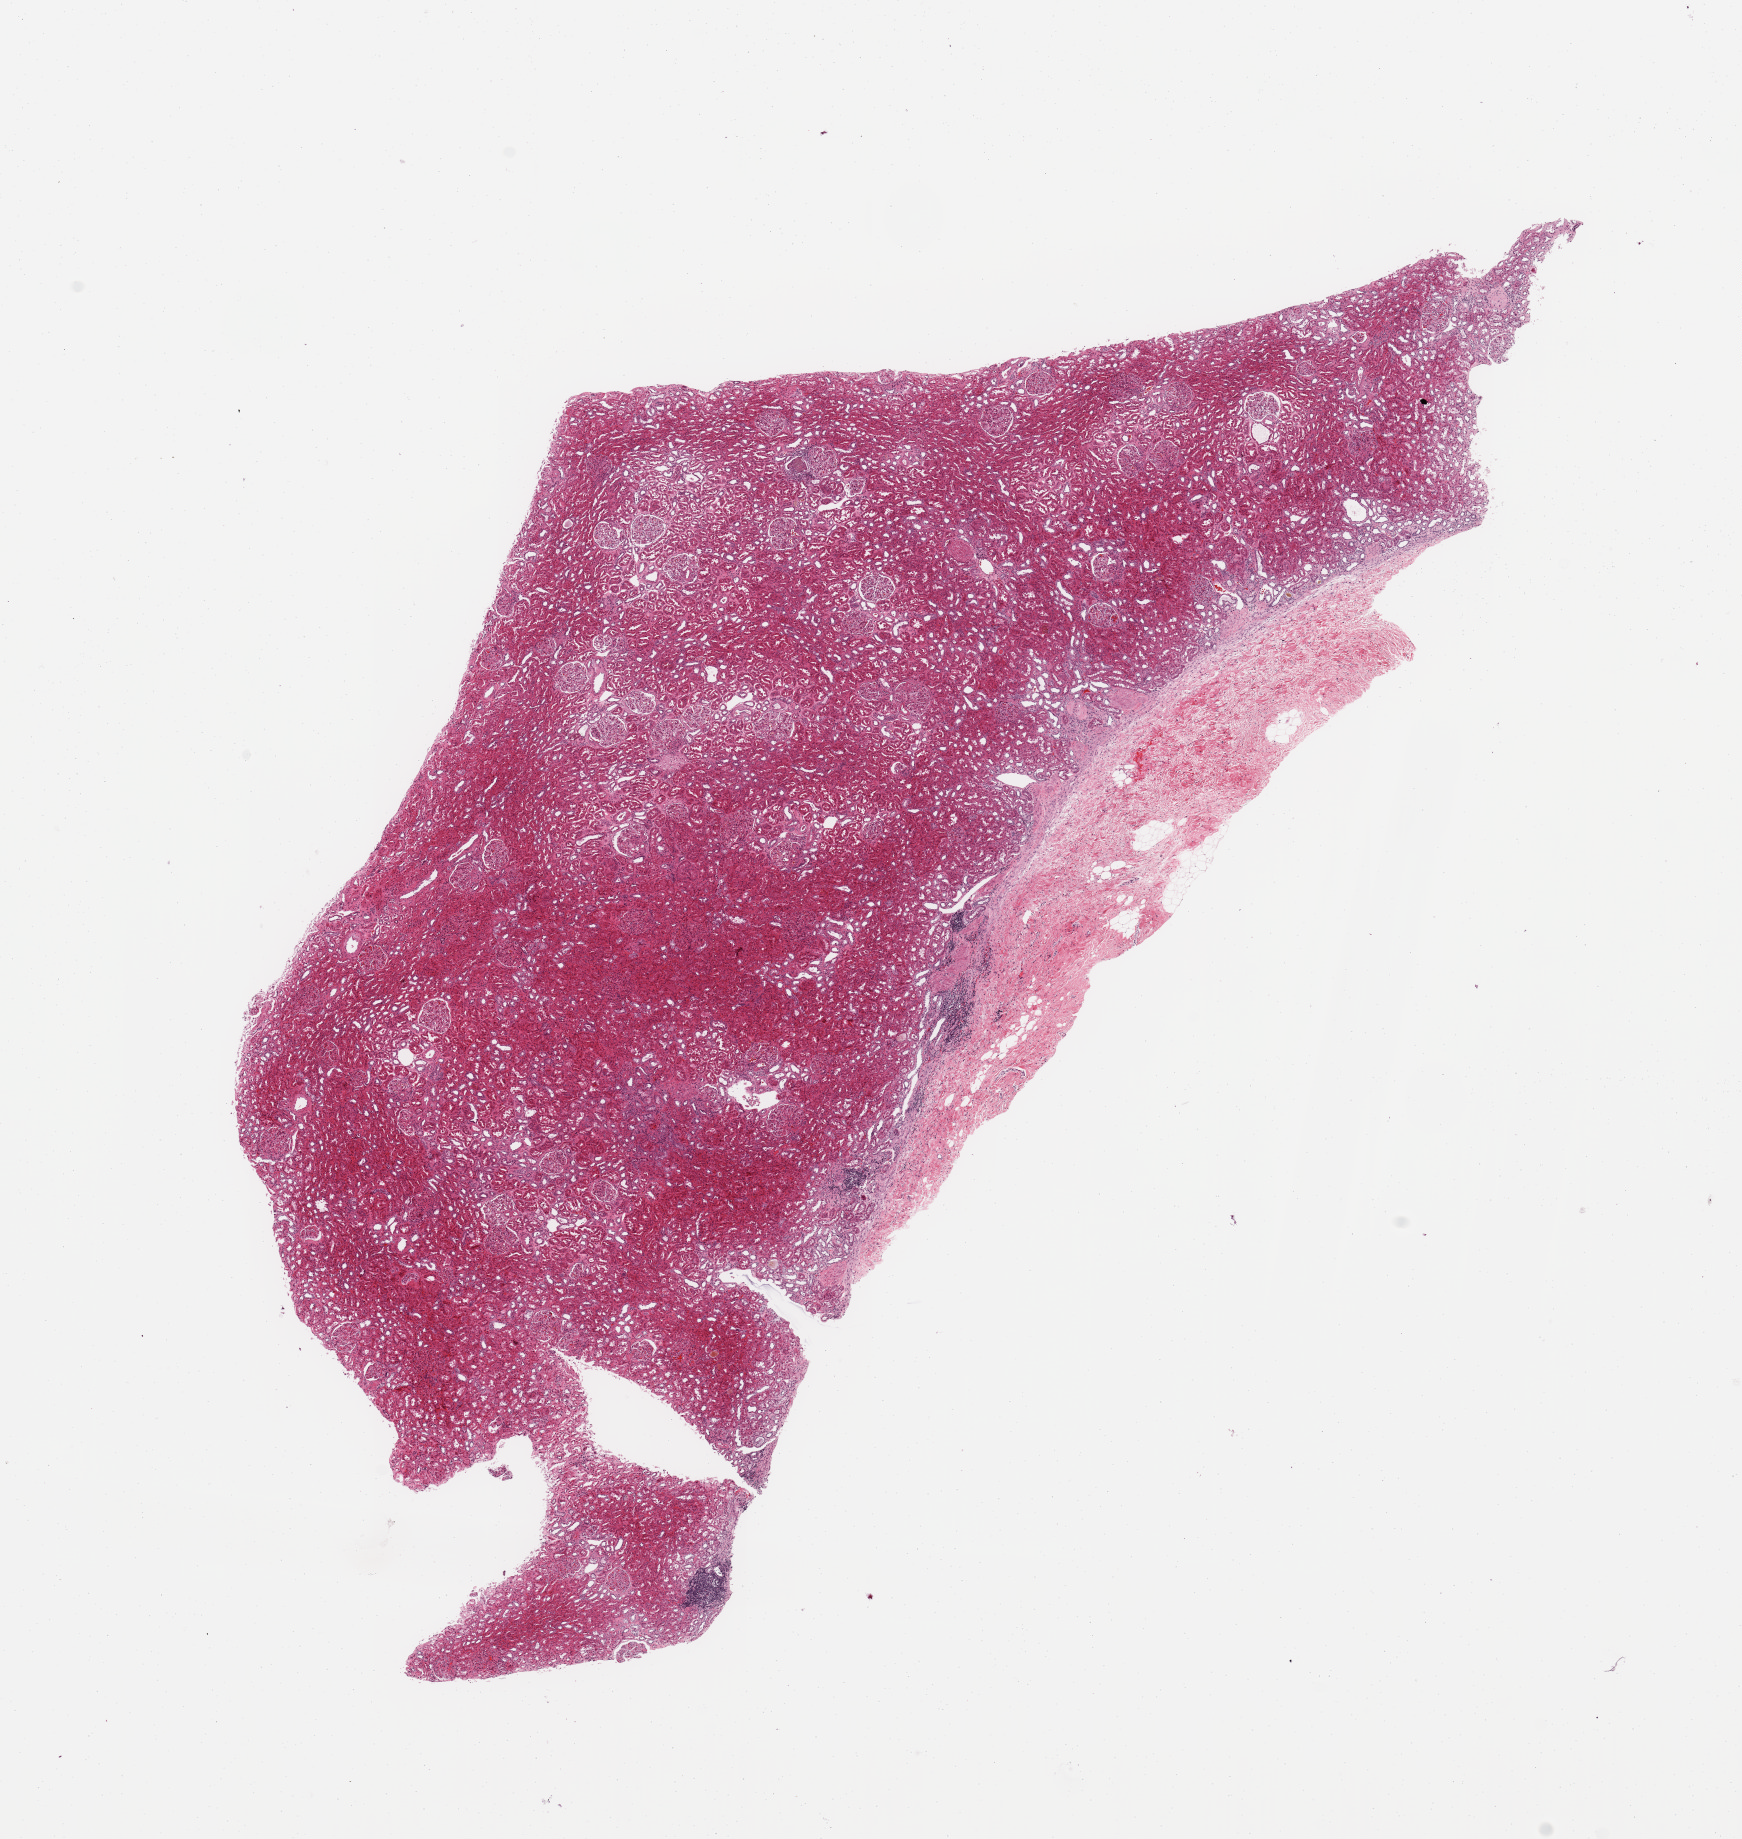
Whole-slide histology image, H&E, whole scanned area (about 13.8 x 14.5 mm, acquisition: 20x scan) shown as a low-resolution overview, normal (non-tumour) tissue sample, sampled site: kidney. Patient: male, age 48 years.
This section: normal (non-tumour) tissue from the same patient. Patient diagnosis: Renal cell carcinoma, NOS.